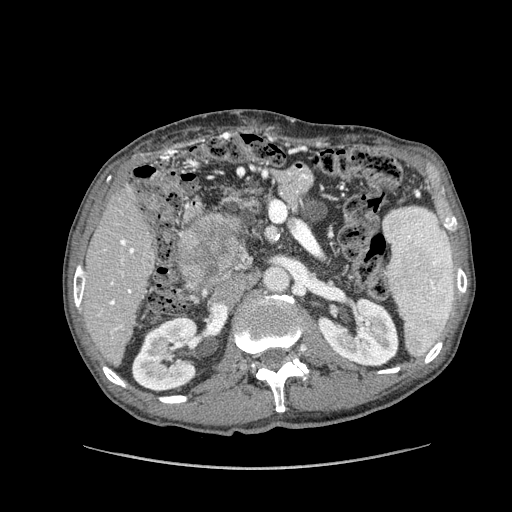
Contrast-enhanced abdominal CT (liver protocol), one axial slice; position 47 of 162 along the scan axis; 100 kVp; soft-tissue window (W 400 / L 40 HU); 2.5 mm slice thickness; 512 × 512 image matrix, field of view 400 × 400 mm. From the clinical record (not read from this slice): diagnosis: hepatocellular carcinoma (patient treated with transarterial chemoembolisation; whether this scan precedes or follows treatment is not stated here); TNM stage (as recorded): Stage-IIIA; Child-Pugh class: A; tumour size: 9.9 cm.
Annotated regions visible in this slice (semi-automatic segmentation, software-assisted and operator-edited):
- liver parenchyma outside the tumour (the mass and vessels are separate outlines, so this box may not span the whole liver): bounding box [x1, y1, x2, y2] px = [80, 184, 156, 364]
- mass: [178, 213, 240, 281]
- liver vessels: [82, 239, 134, 330]